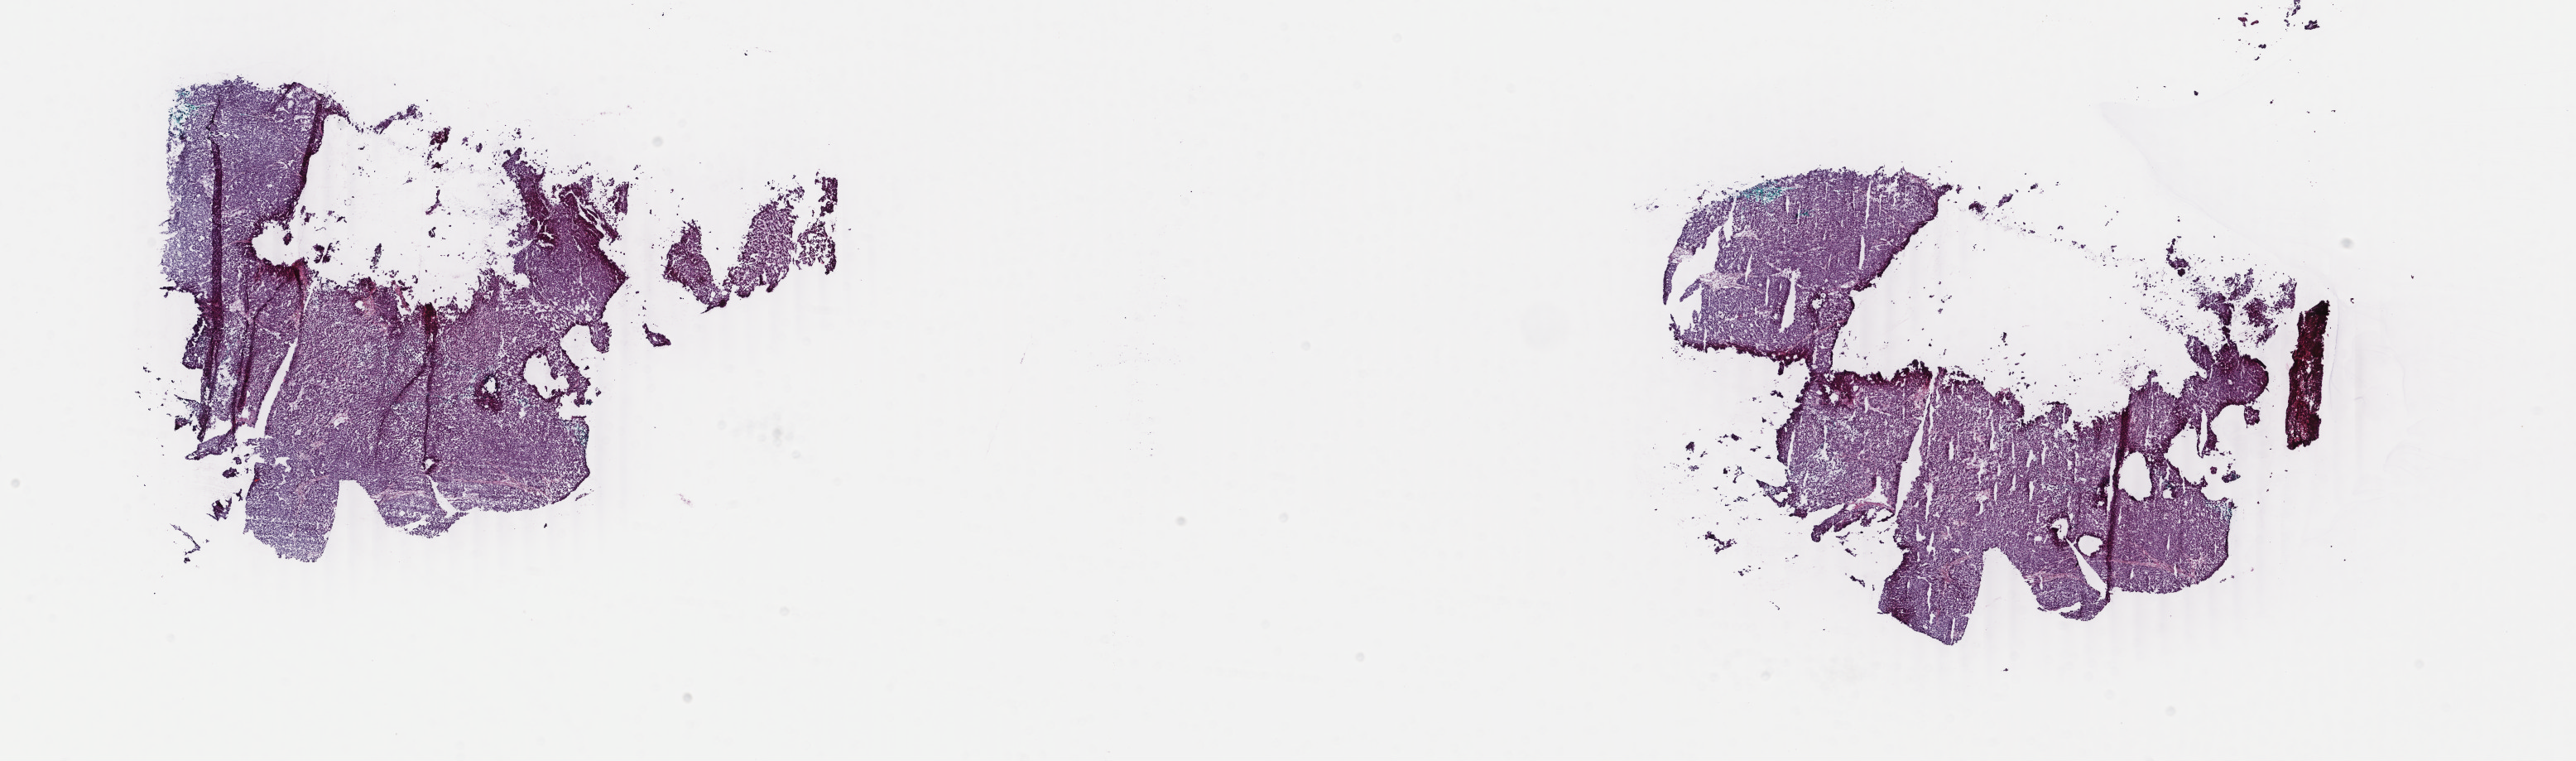
Whole-slide histology image, Hematoxylin and eosin (H&E) stained — low-resolution overview of the scanned area, about 24.7 x 7.3 mm (slide scanned at 40x), frozen section from the bottom of the tissue portion, sample: primary tumour, liver. Patient: male, age at initial diagnosis 62 years. Histologic grade: G1 (well differentiated). Slide review estimates, as recorded: tumour cells 93%, tumour nuclei 95%, normal cells 0%, stromal cells 5%, necrosis 2%. Infiltration values recorded for this section: lymphocyte infiltration 1%, monocyte infiltration 1%, neutrophil infiltration 0%.
TNM: T1 NX MX. Histologic diagnosis: Hepatocellular carcinoma, NOS. AJCC pathologic stage: I (7th edition).